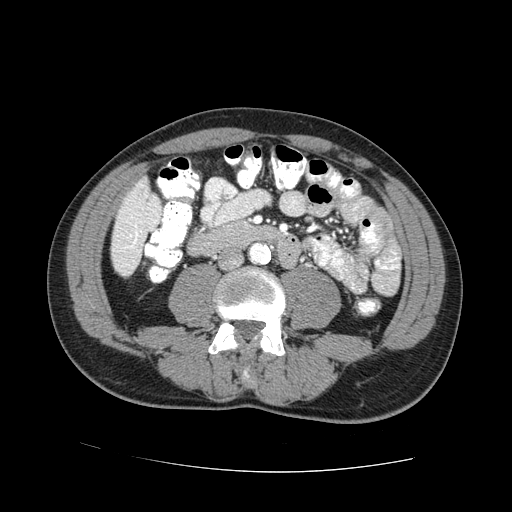
Contrast-enhanced abdominal CT (liver protocol), one axial slice. Slice 8 of 73 in the series (ordered by position). 100 kVp. One of 2 acquisitions stored at this slice position. Soft-tissue window (W 400 / L 40 HU). 2.5 mm slice thickness. 512 × 512 image matrix. Case-level facts recorded for this patient, not image findings: diagnosis: hepatocellular carcinoma (patient treated with transarterial chemoembolisation; whether this scan precedes or follows treatment is not stated here); TNM stage (as recorded): Stage-IVA; Child-Pugh class: A; tumour differentiation: no biopsy.
Structures marked on this image (semi-automatic segmentation, software-assisted and operator-edited):
- liver parenchyma outside the tumour (the mass and vessels are separate outlines, so this box may not span the whole liver): bounding box (x1, y1, x2, y2) in pixels: (112, 176, 160, 276)
- liver vessels: (133, 225, 138, 244)